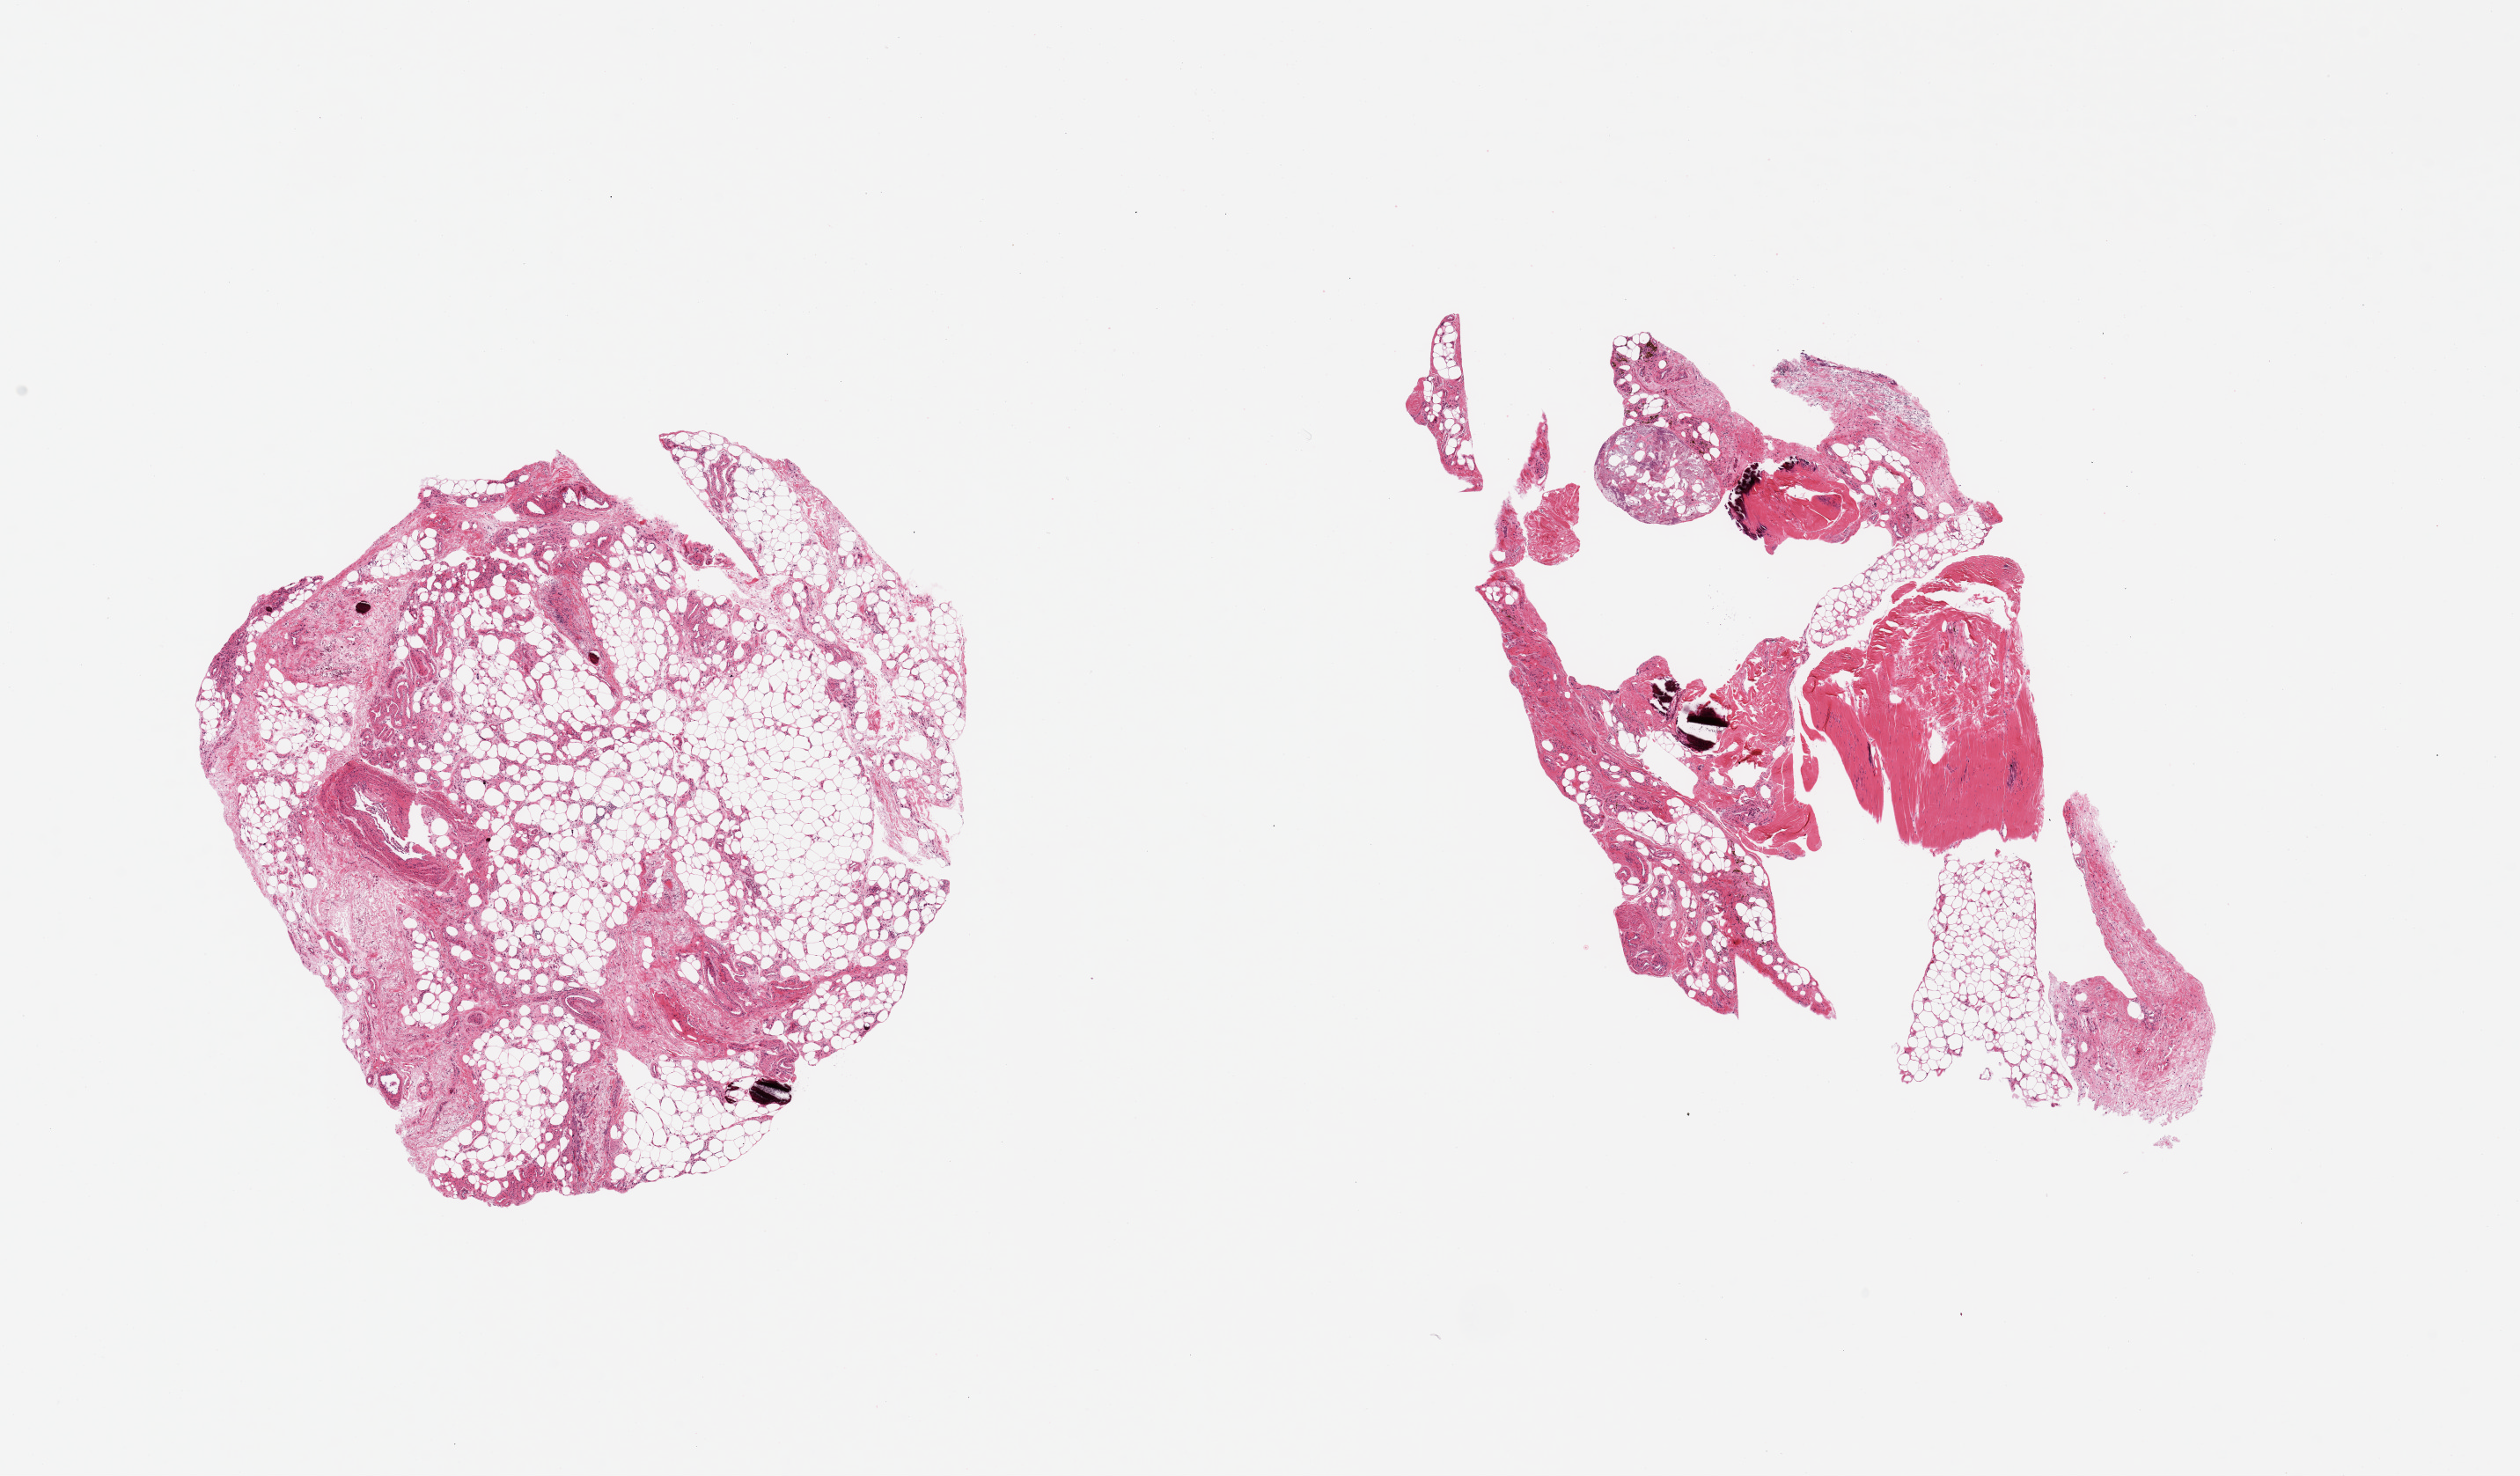
Digitized H&E-stained section, a low-resolution overview of the entire scanned area, about 22.6 x 13.3 mm; PAXgene-fixed, paraffin-embedded tissue; section of adipose tissue (target tissue); donor tissue sample. Female donor.
- reviewer comment on this tissue sample: 2 pieces; 1 with 25% fibrous content; other with 30% fascia, 30% fibrous stroma; calcium deposits in both